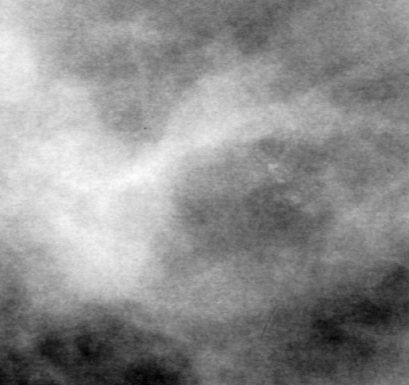
Cropped region of a digitized screen-film mammogram centred on a radiologist-marked abnormality, left breast, MLO view.
Calcifications, morphology amorphous, distribution clustered; BI-RADS assessment category 4; subtlety rating 2 on a 1 (subtle) to 5 (obvious) scale; pathology result (as recorded, not read from the image): benign.